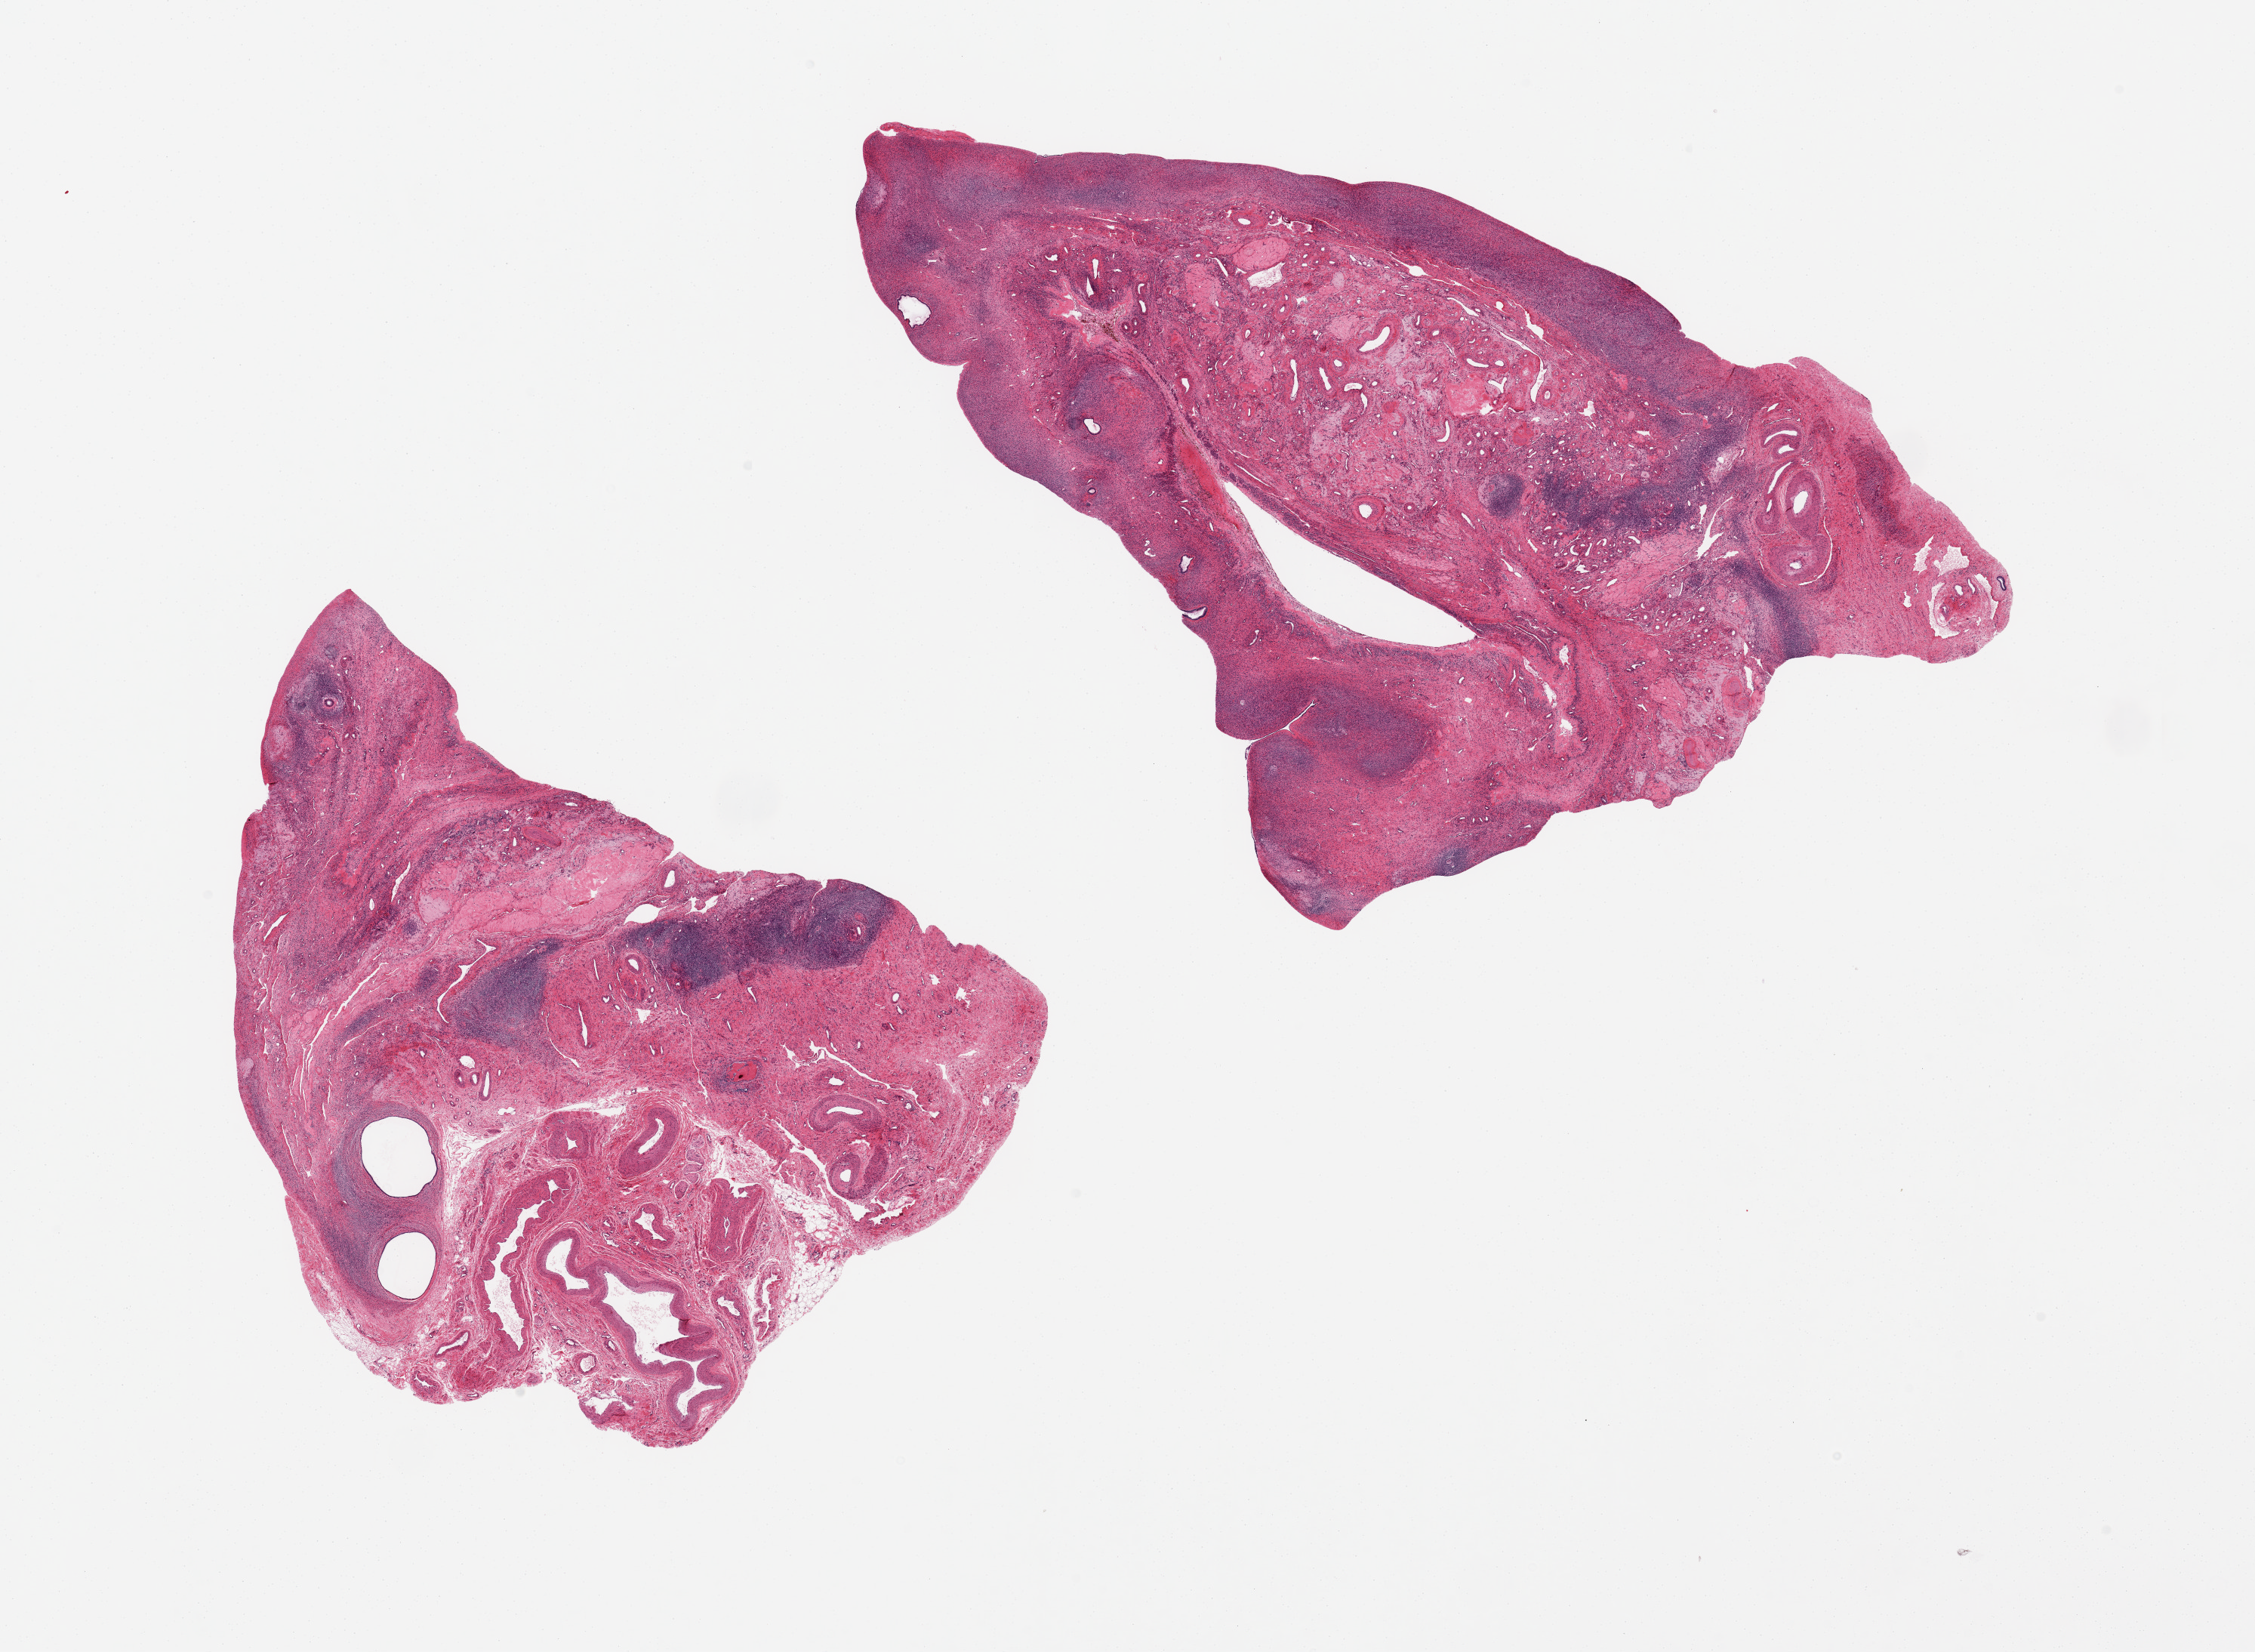
Digitized hematoxylin and eosin (H&E)-stained section, shown as a low-resolution overview of the whole scanned area (about 23.6 x 17.3 mm); PAXgene-fixed, paraffin-embedded tissue; sampled site (target tissue): ovary; tissue donor sample. Female donor.
Reviewer comment on this tissue sample: 2 pieces, 9x7 & 13x8mm; typical post menopausal appearance.